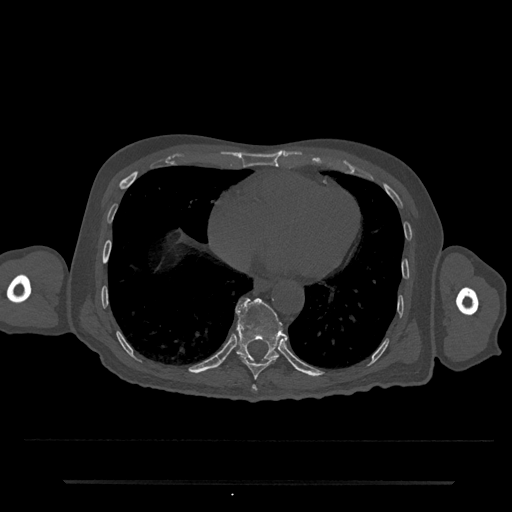
CT including the spine, one axial slice; slice 341 of 797 in the series (ordered by position); 120 kVp; bone window (W 1800 / L 400 HU); 0.5 mm slice thickness; 512 × 512 image matrix. Male patient, age 74 years. From the clinical record (not read from this slice): primary cancer: prostate.
Structures marked on this image (semi-automatically segmented with operator editing):
- T10 vertebra: bounding box [x1, y1, x2, y2] px = [235, 298, 285, 361]
- T8 vertebra: [252, 385, 257, 391]
- T9 vertebra: [239, 355, 277, 380]